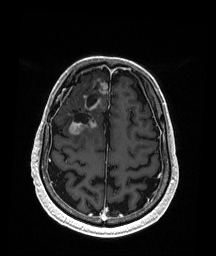
Brain MRI from a brain-tumour surgery series, one axial slice; slice 55 of 192 in the series (ordered by position); T1-weighted post-contrast; 1 mm slice thickness; 216 × 256 image matrix. Case-level facts recorded for this patient, not image findings: histopathology: Astrocytoma; WHO grade: 3; IDH mutation: yes.
Structures marked on this image (manually delineated by an expert):
- previous resection cavity: bounding box (x1, y1, x2, y2) in pixels: (69, 93, 99, 124)
- tumour: (69, 83, 108, 136)